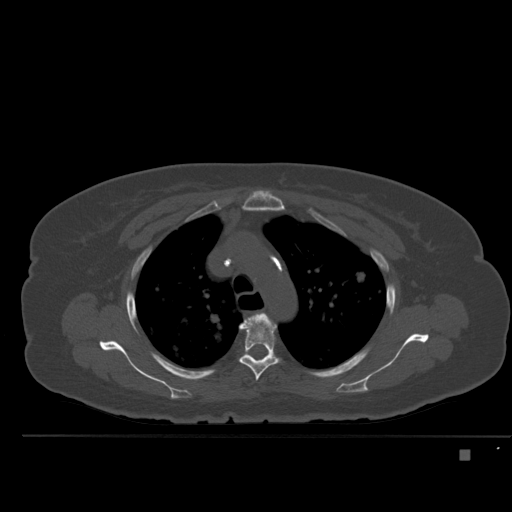
CT including the spine, one axial slice. Position 367 of 477 along the scan axis. Bone window (W 1800 / L 400 HU). 1.5 mm slice thickness. 512 × 512 image matrix, field of view 422 × 422 mm. Female patient, age 74 years. From the clinical record (not read from this slice): primary cancer: colon.
Structures marked on this image (semi-automatic segmentation, software-assisted and operator-edited):
- T3 vertebra: bounding box <251,313,277,329> (left, top, right, bottom; pixels)
- T4 vertebra: <239,313,279,381>